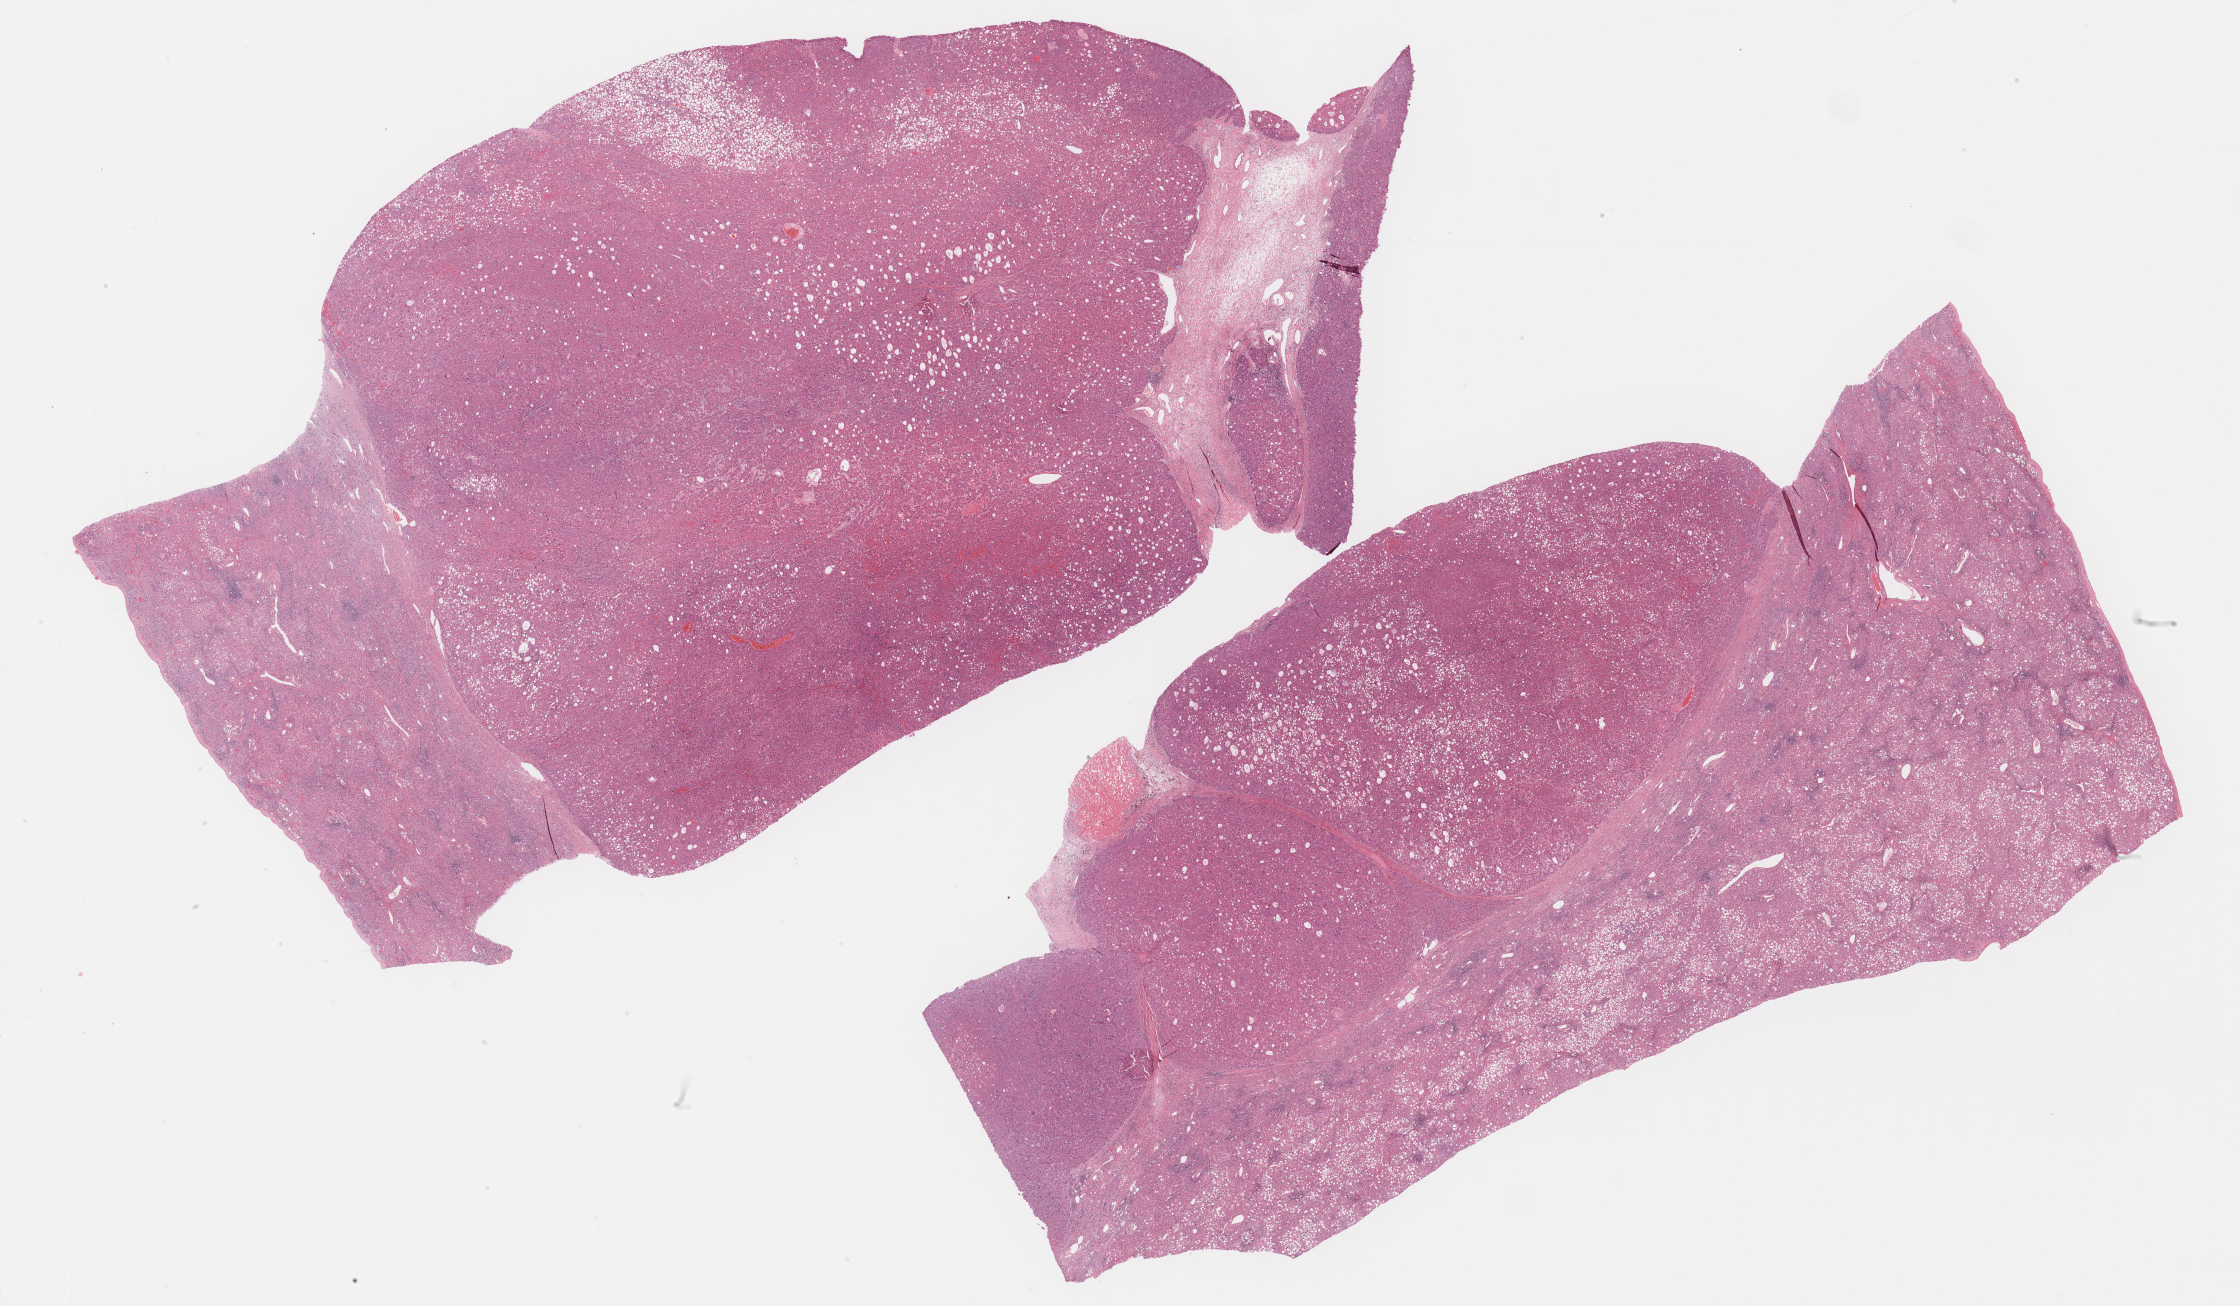
Digitized Hematoxylin and eosin (H&E) stained tissue section (whole slide), shown as a low-resolution overview of the whole scanned area (about 36.2 x 21.1 mm); formalin-fixed paraffin-embedded (FFPE) diagnostic section; liver, primary tumour sample. Male, age 65 years at initial diagnosis. Histologic grade: G1 (well differentiated).
Histologic diagnosis: Hepatocellular carcinoma, NOS. AJCC pathologic stage: I.